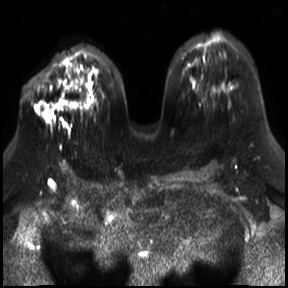
Breast MRI, one axial slice. Position 18 of 30 along the scan axis. Diffusion-weighted series; image 2 of 4 stored at this slice position (different b-values; order by instance number). 3 T. 4 mm slice thickness. 288 × 288 image matrix, field of view 340 × 340 mm. Female patient.
Structures marked on this image (manually delineated by an expert):
- tumour on diffusion-weighted imaging: bounding box [x1, y1, x2, y2] px = [36, 102, 67, 120]